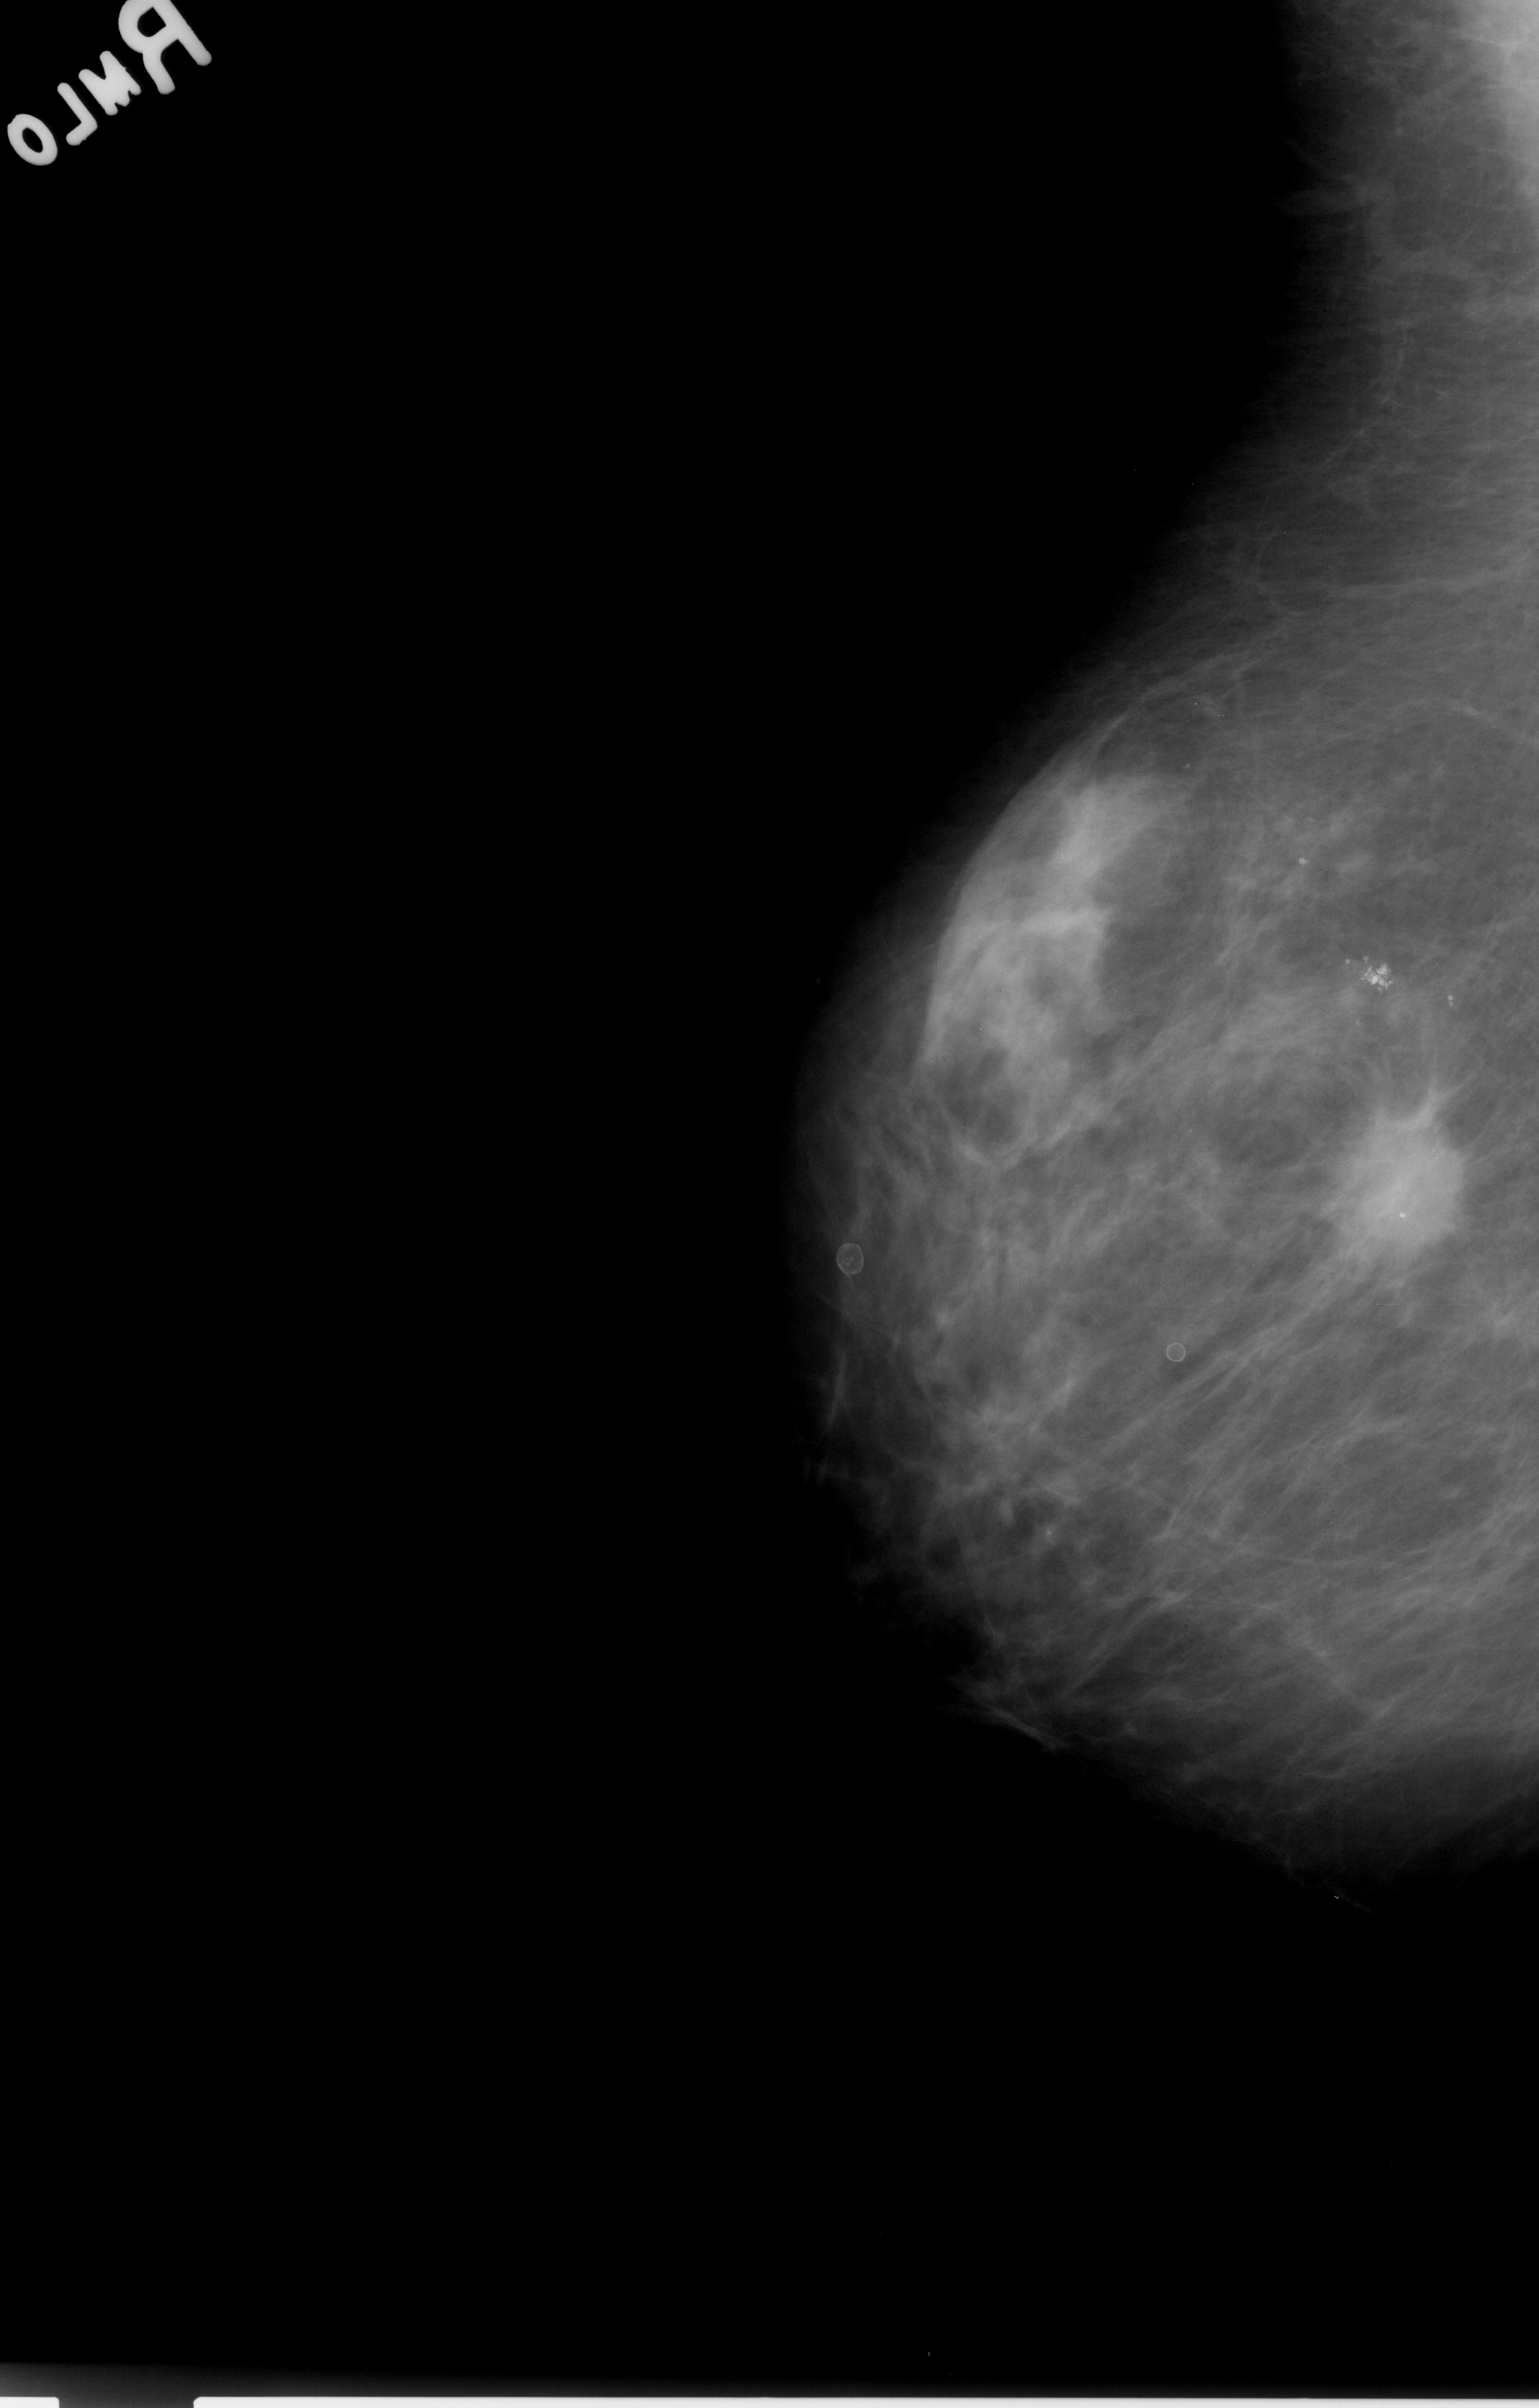
Digitized screen-film mammogram; right breast; MLO view; 1539 × 2408 image matrix.
Expert-marked regions of interest on this image (one box per marked abnormality):
- mass, shape irregular / architectural distortion, margins spiculated; BI-RADS assessment category 4; pathology result (as recorded, not read from the image): malignant: bounding box (x1, y1, x2, y2) in pixels: (1333, 1095, 1471, 1256)